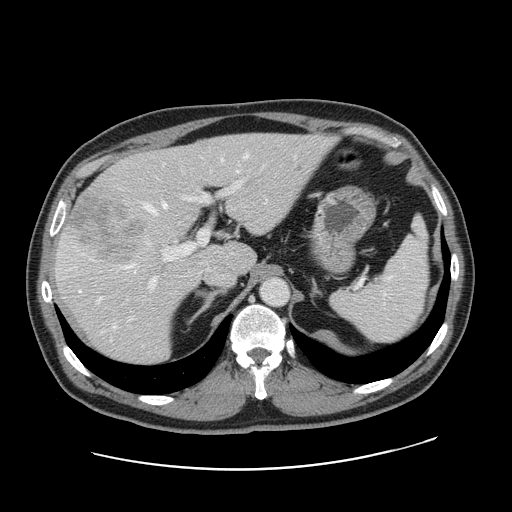
Contrast-enhanced abdominal CT, one axial slice; slice 112 of 178 in the series (ordered by position); 120 kVp; intravenous contrast given; soft-tissue window (W 400 / L 40 HU); 2.5 mm slice thickness; 512 × 512 image matrix, field of view 403 × 403 mm. Male patient, age 63 years. From the clinical record (not read from this slice): diagnosis: colorectal cancer liver metastases, imaged before liver resection; multiple liver metastases: yes; largest metastasis: 8 cm; disease in both lobes: yes.
Structures marked on this image (manually delineated by an expert):
- hepatic veins: bounding box [x1, y1, x2, y2] px = [79, 154, 248, 327]
- liver: [52, 134, 330, 366]
- planned liver remnant (the part of the liver to remain after resection): [133, 134, 330, 274]
- portal vein (with intrahepatic branches): [148, 180, 243, 289]
- liver metastasis: [298, 165, 304, 171]
- liver metastasis: [69, 196, 142, 268]